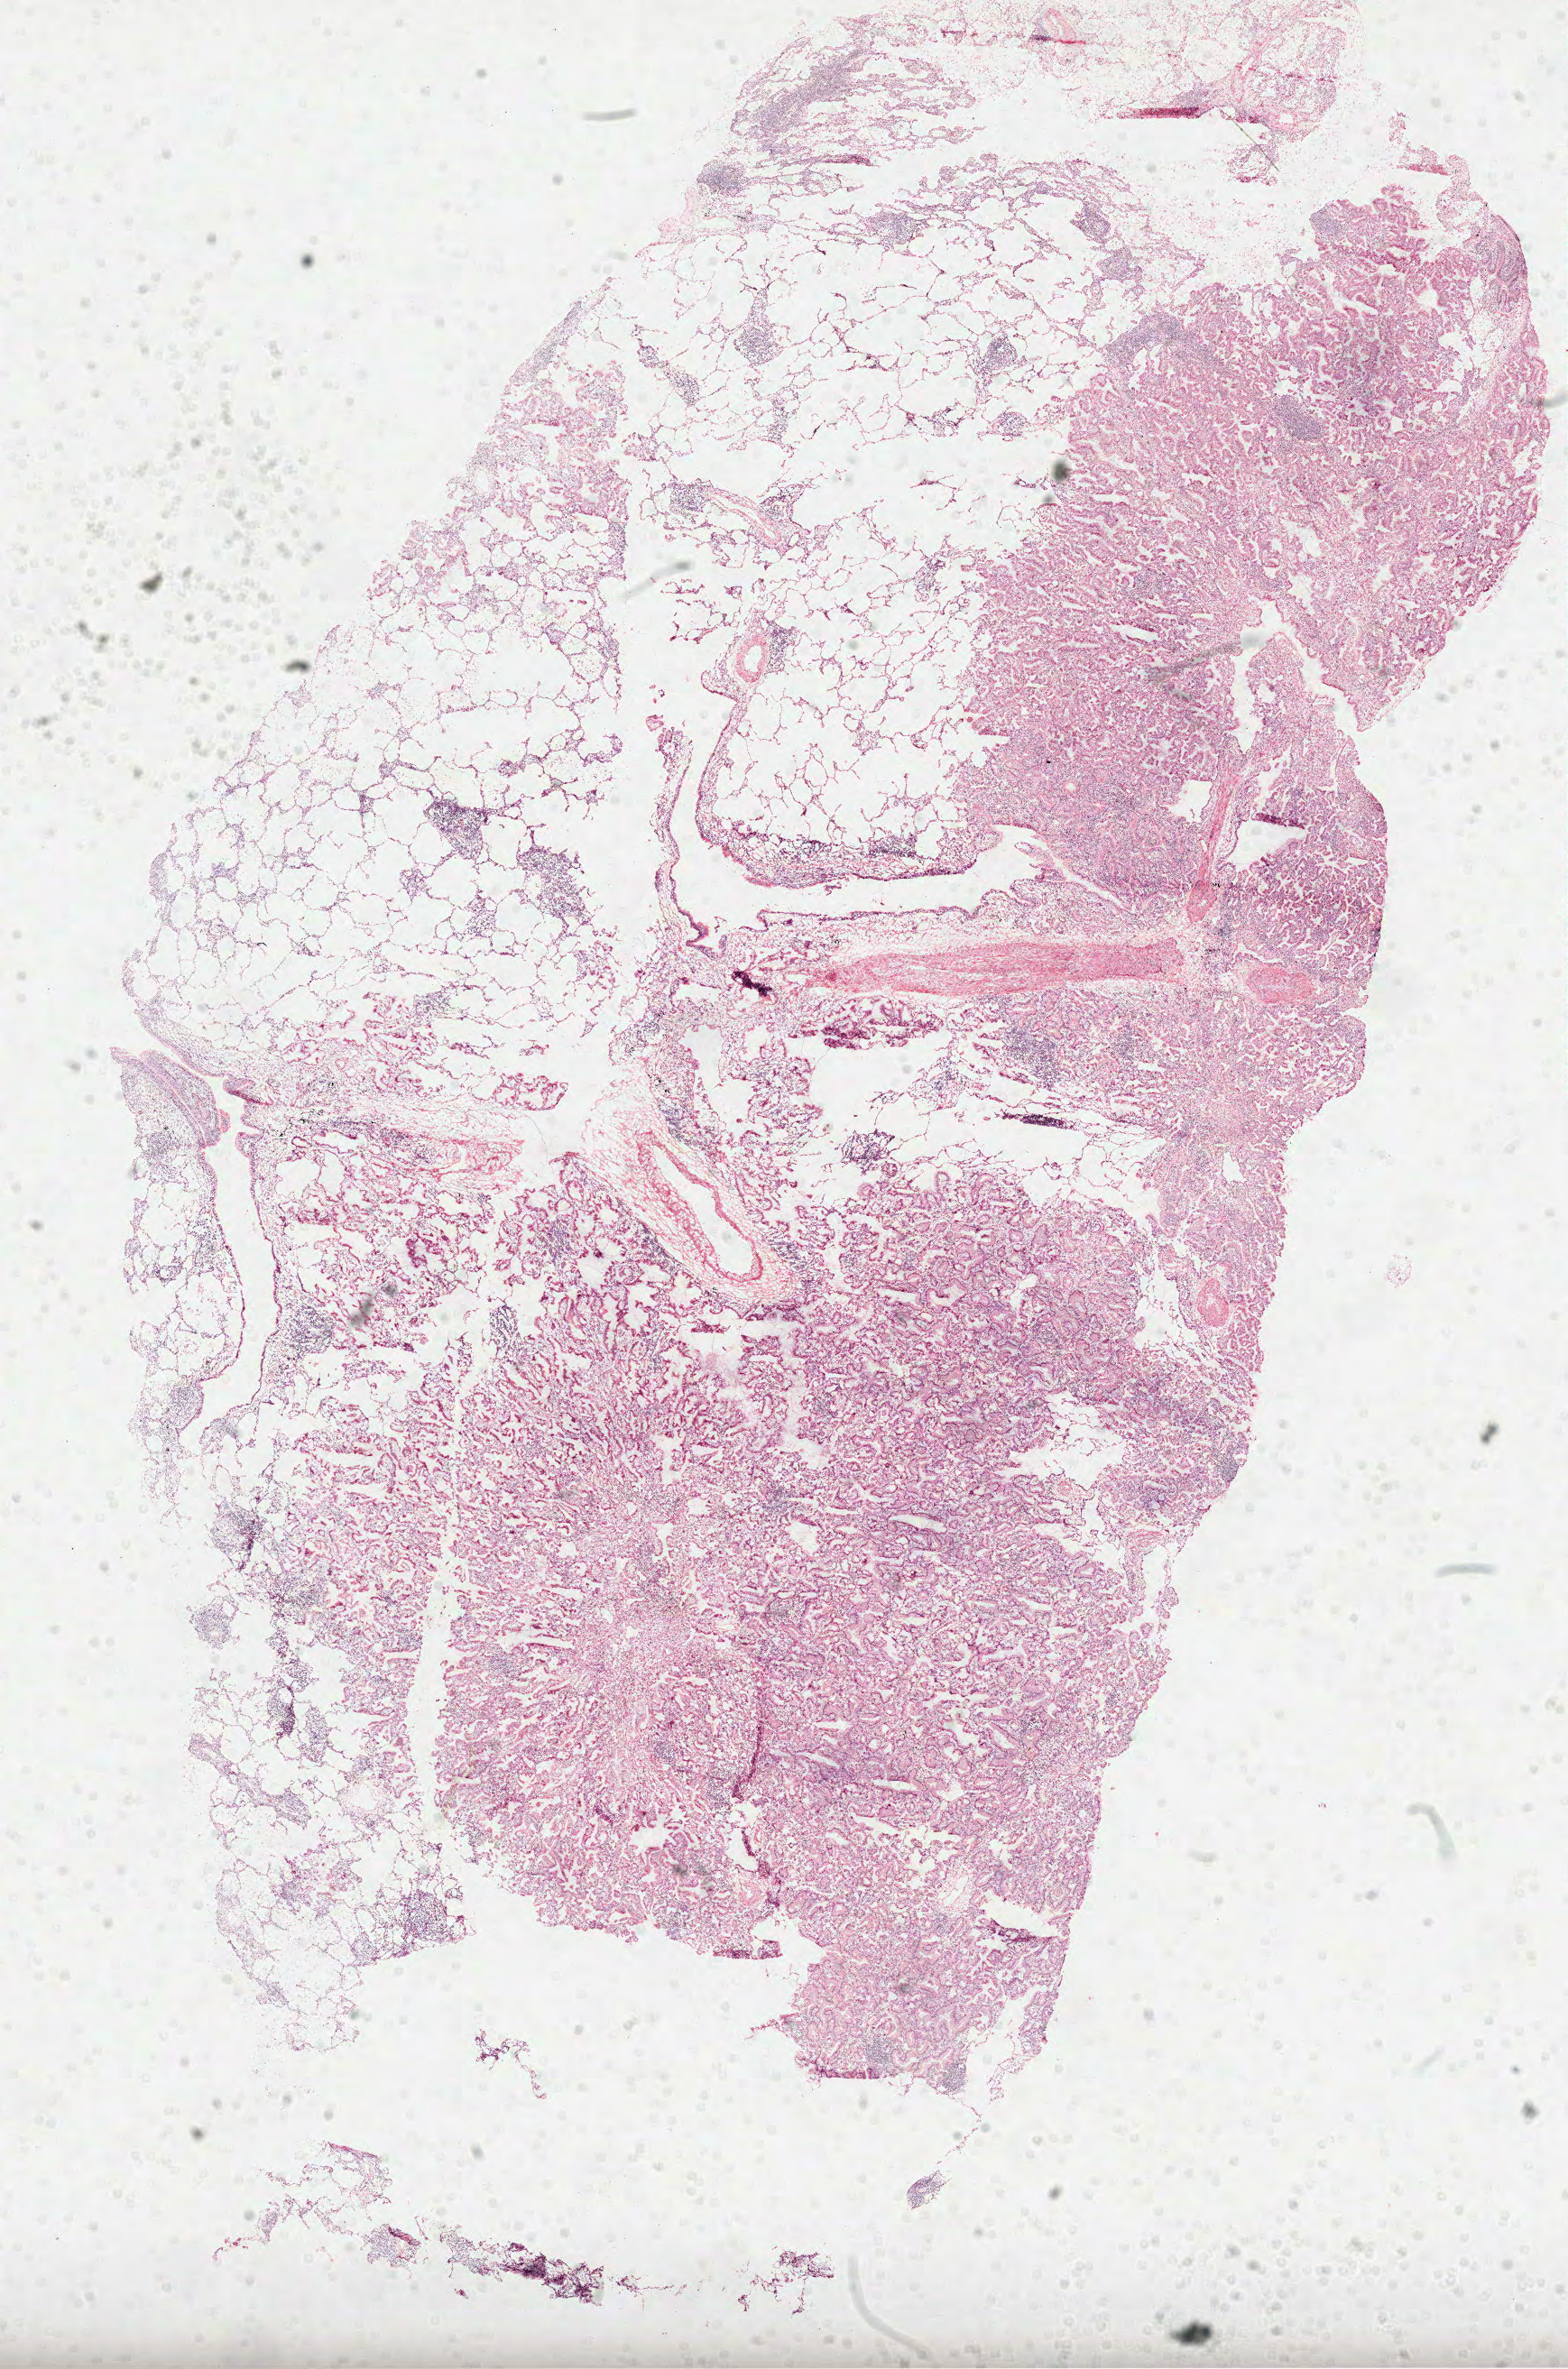
H&E-stained whole-slide image — whole scanned area (about 14.0 x 21.2 mm, acquisition: 40x scan) shown as a low-resolution overview; frozen section; sample: primary tumour, lung. Male patient; age at initial diagnosis 70 years. Slide review estimates, as recorded: tumour cells 75%, tumour nuclei 60%, normal cells 25%, stromal cells 0%, necrosis 0%. Inflammatory infiltration, as recorded: lymphocyte infiltration 25%.
• AJCC pathologic stage: IB (6th edition)
• pathologic diagnosis: Bronchio-alveolar carcinoma, mucinous (lower lobe, lung)
• laterality: left